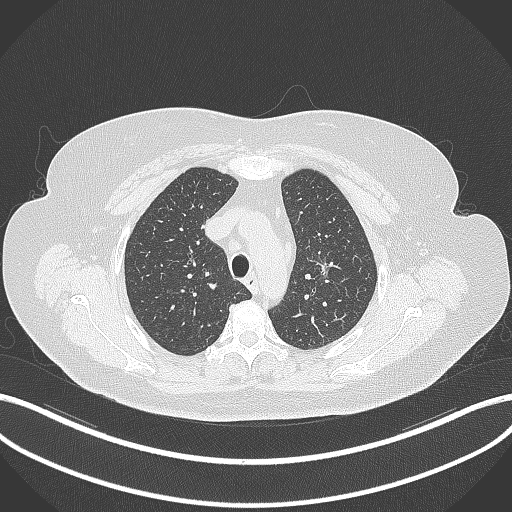
Chest CT, one axial slice; slice 258 of 309 in the series (ordered by position); reconstruction kernel B70f; lung window (W 1500 / L -600 HU); 1 mm slice thickness; 512 × 512 image matrix, field of view 400 × 400 mm. Female patient, age 70 years. From the clinical record (not read from this slice): clinical TNM (as recorded): T1c N0 M0.
Structures marked on this image (rectangle marked by the reading radiologist):
- lung tumour (recorded histology: adenocarcinoma): bounding box <312,253,337,282> (left, top, right, bottom; pixels)